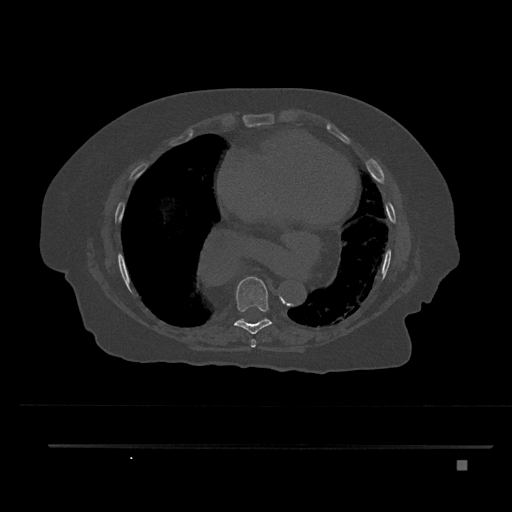
CT including the spine, one axial slice. Position 438 of 797 along the scan axis. Reconstruction kernel Br40s/3. 120 kVp. Bone window (W 1800 / L 400 HU). 0.5 mm slice thickness. 512 × 512 image matrix. Female patient, age 76 years. From the clinical record (not read from this slice): primary cancer: lung.
Structures marked on this image (semi-automatically segmented with operator editing):
- T7 vertebra: bounding box <250,339,256,348> (left, top, right, bottom; pixels)
- T8 vertebra: <234,277,272,334>
- T9 vertebra: <240,319,242,321>